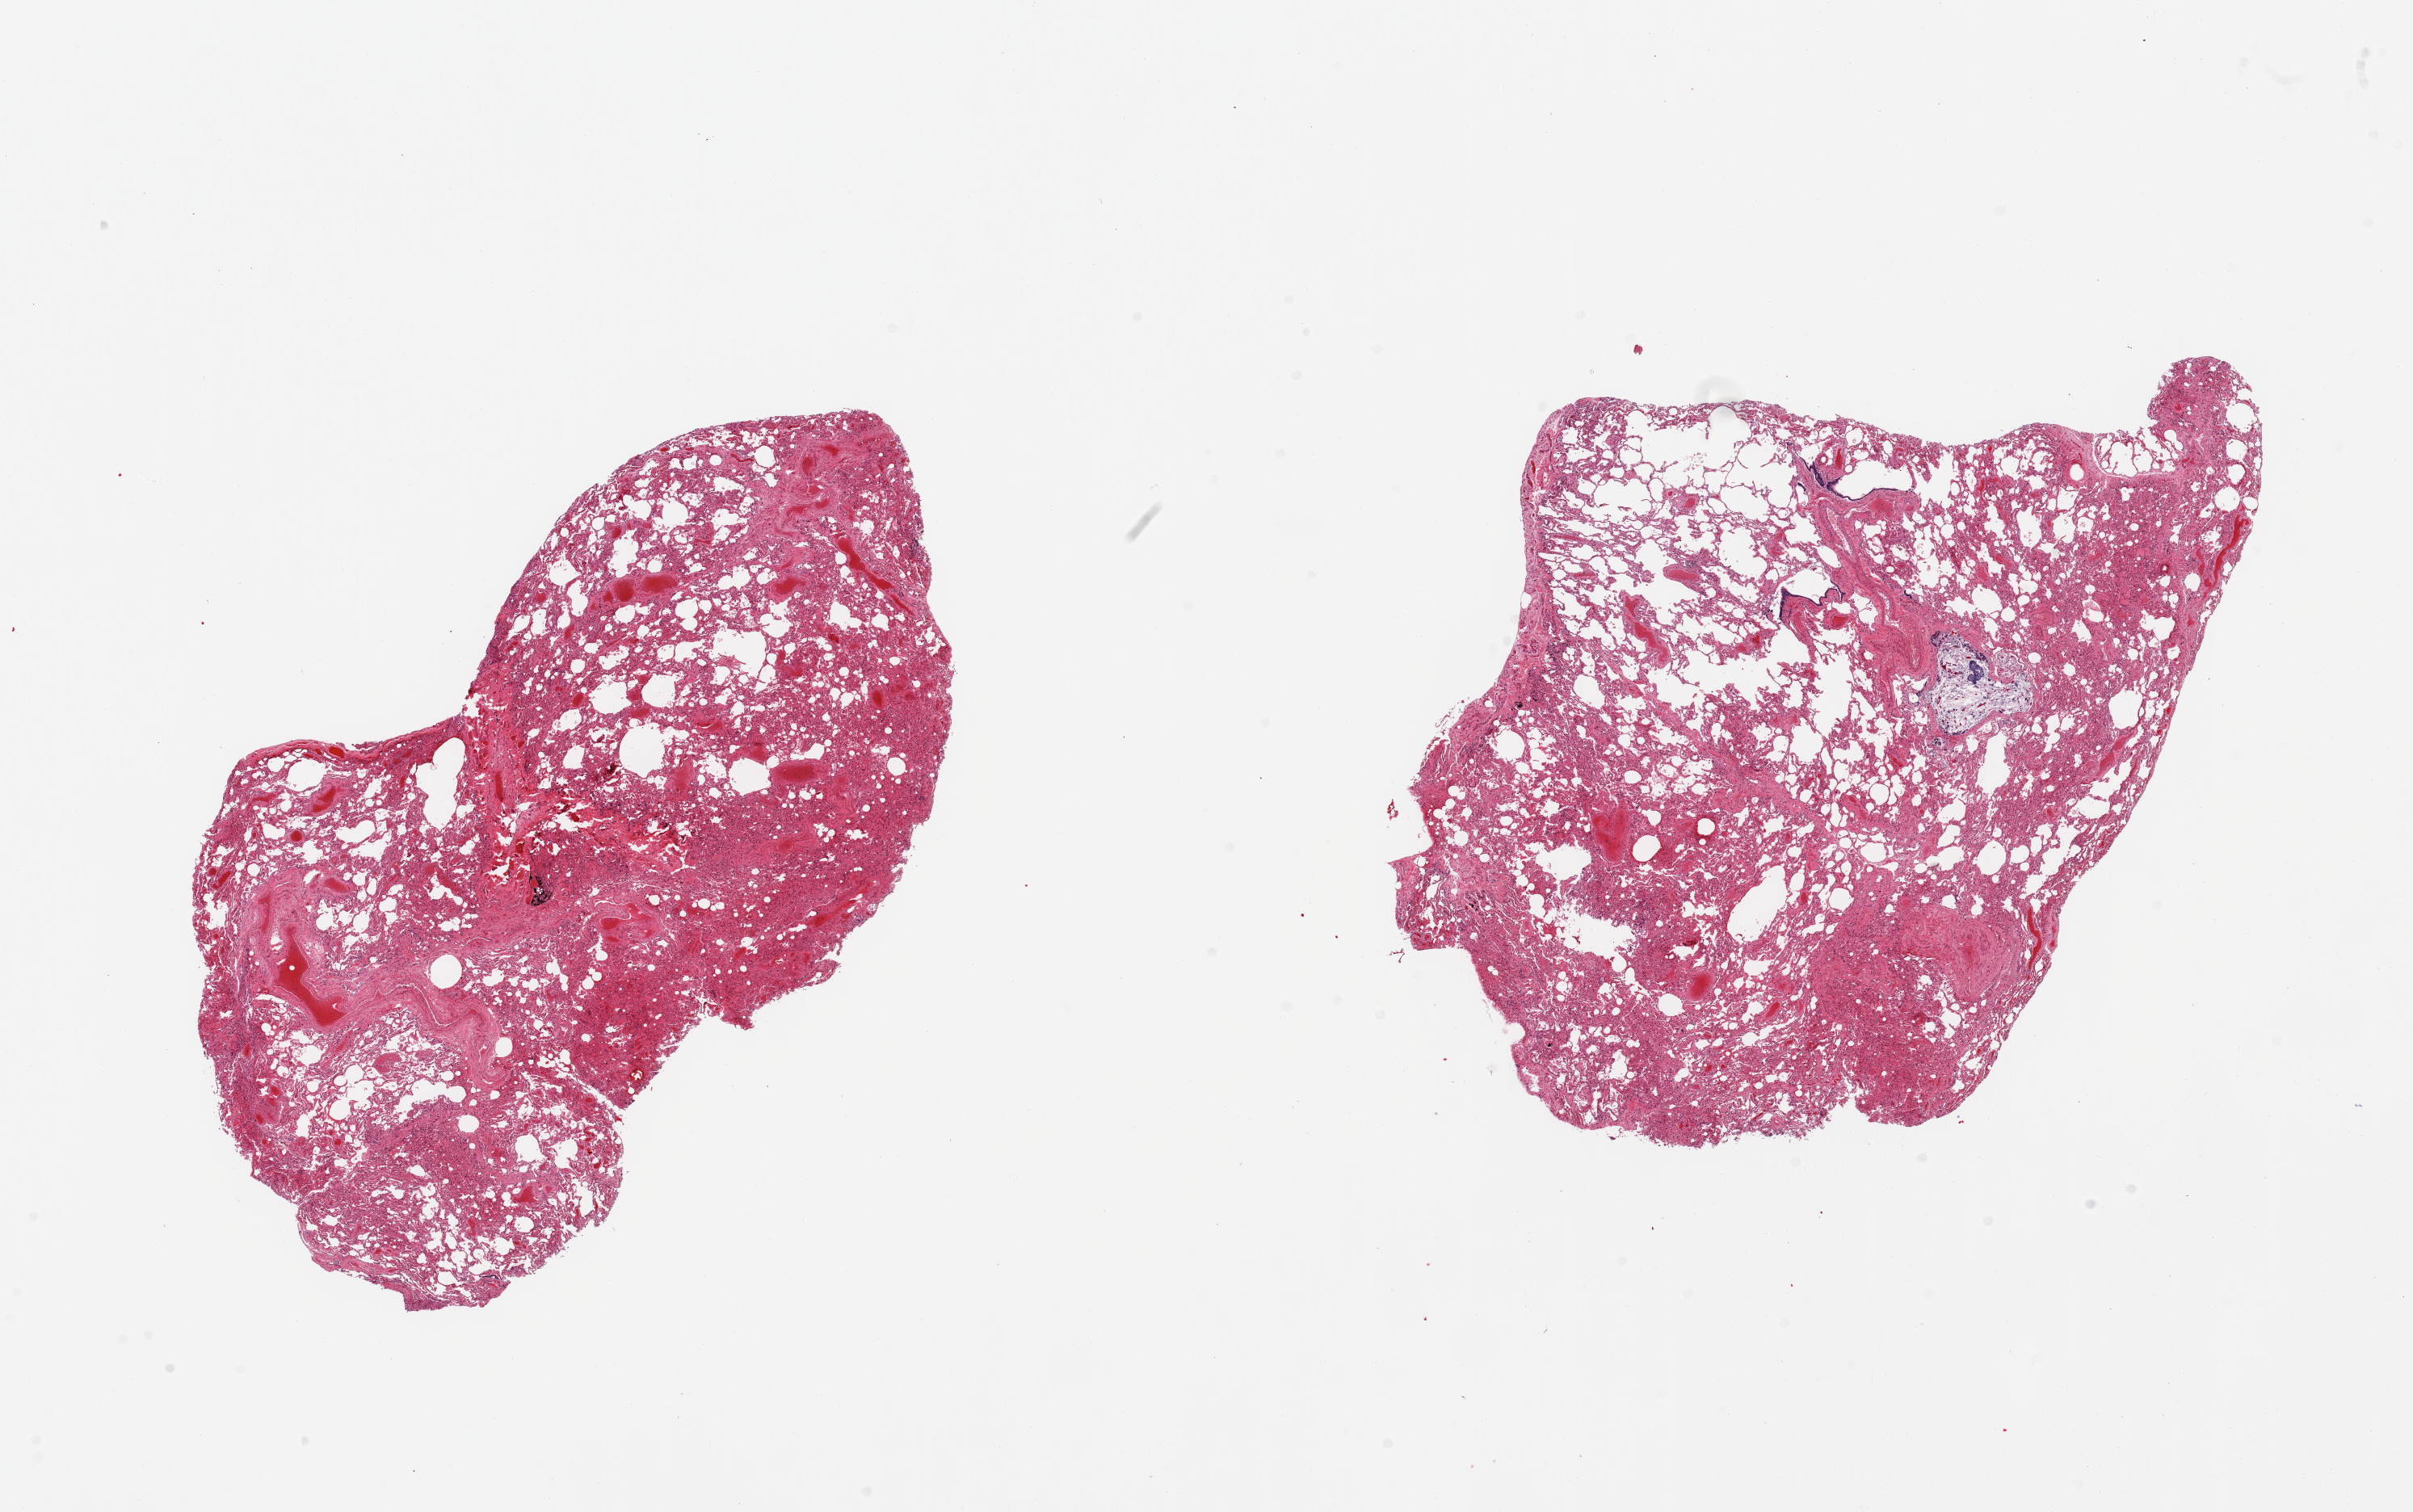
H&E whole-slide image — a low-resolution overview of the entire scanned area, about 23.6 x 14.8 mm. PAXgene-fixed, paraffin-embedded tissue. Section of lung (target tissue). Tissue donor sample. Male donor.
* reviewer comment on this tissue sample: 2 pieces; marked congestion with focal areas of collapsed alveoli; bronchial lumen filled with mucus, desquamated epithelial lining cells, microorganisms and vegetable matter